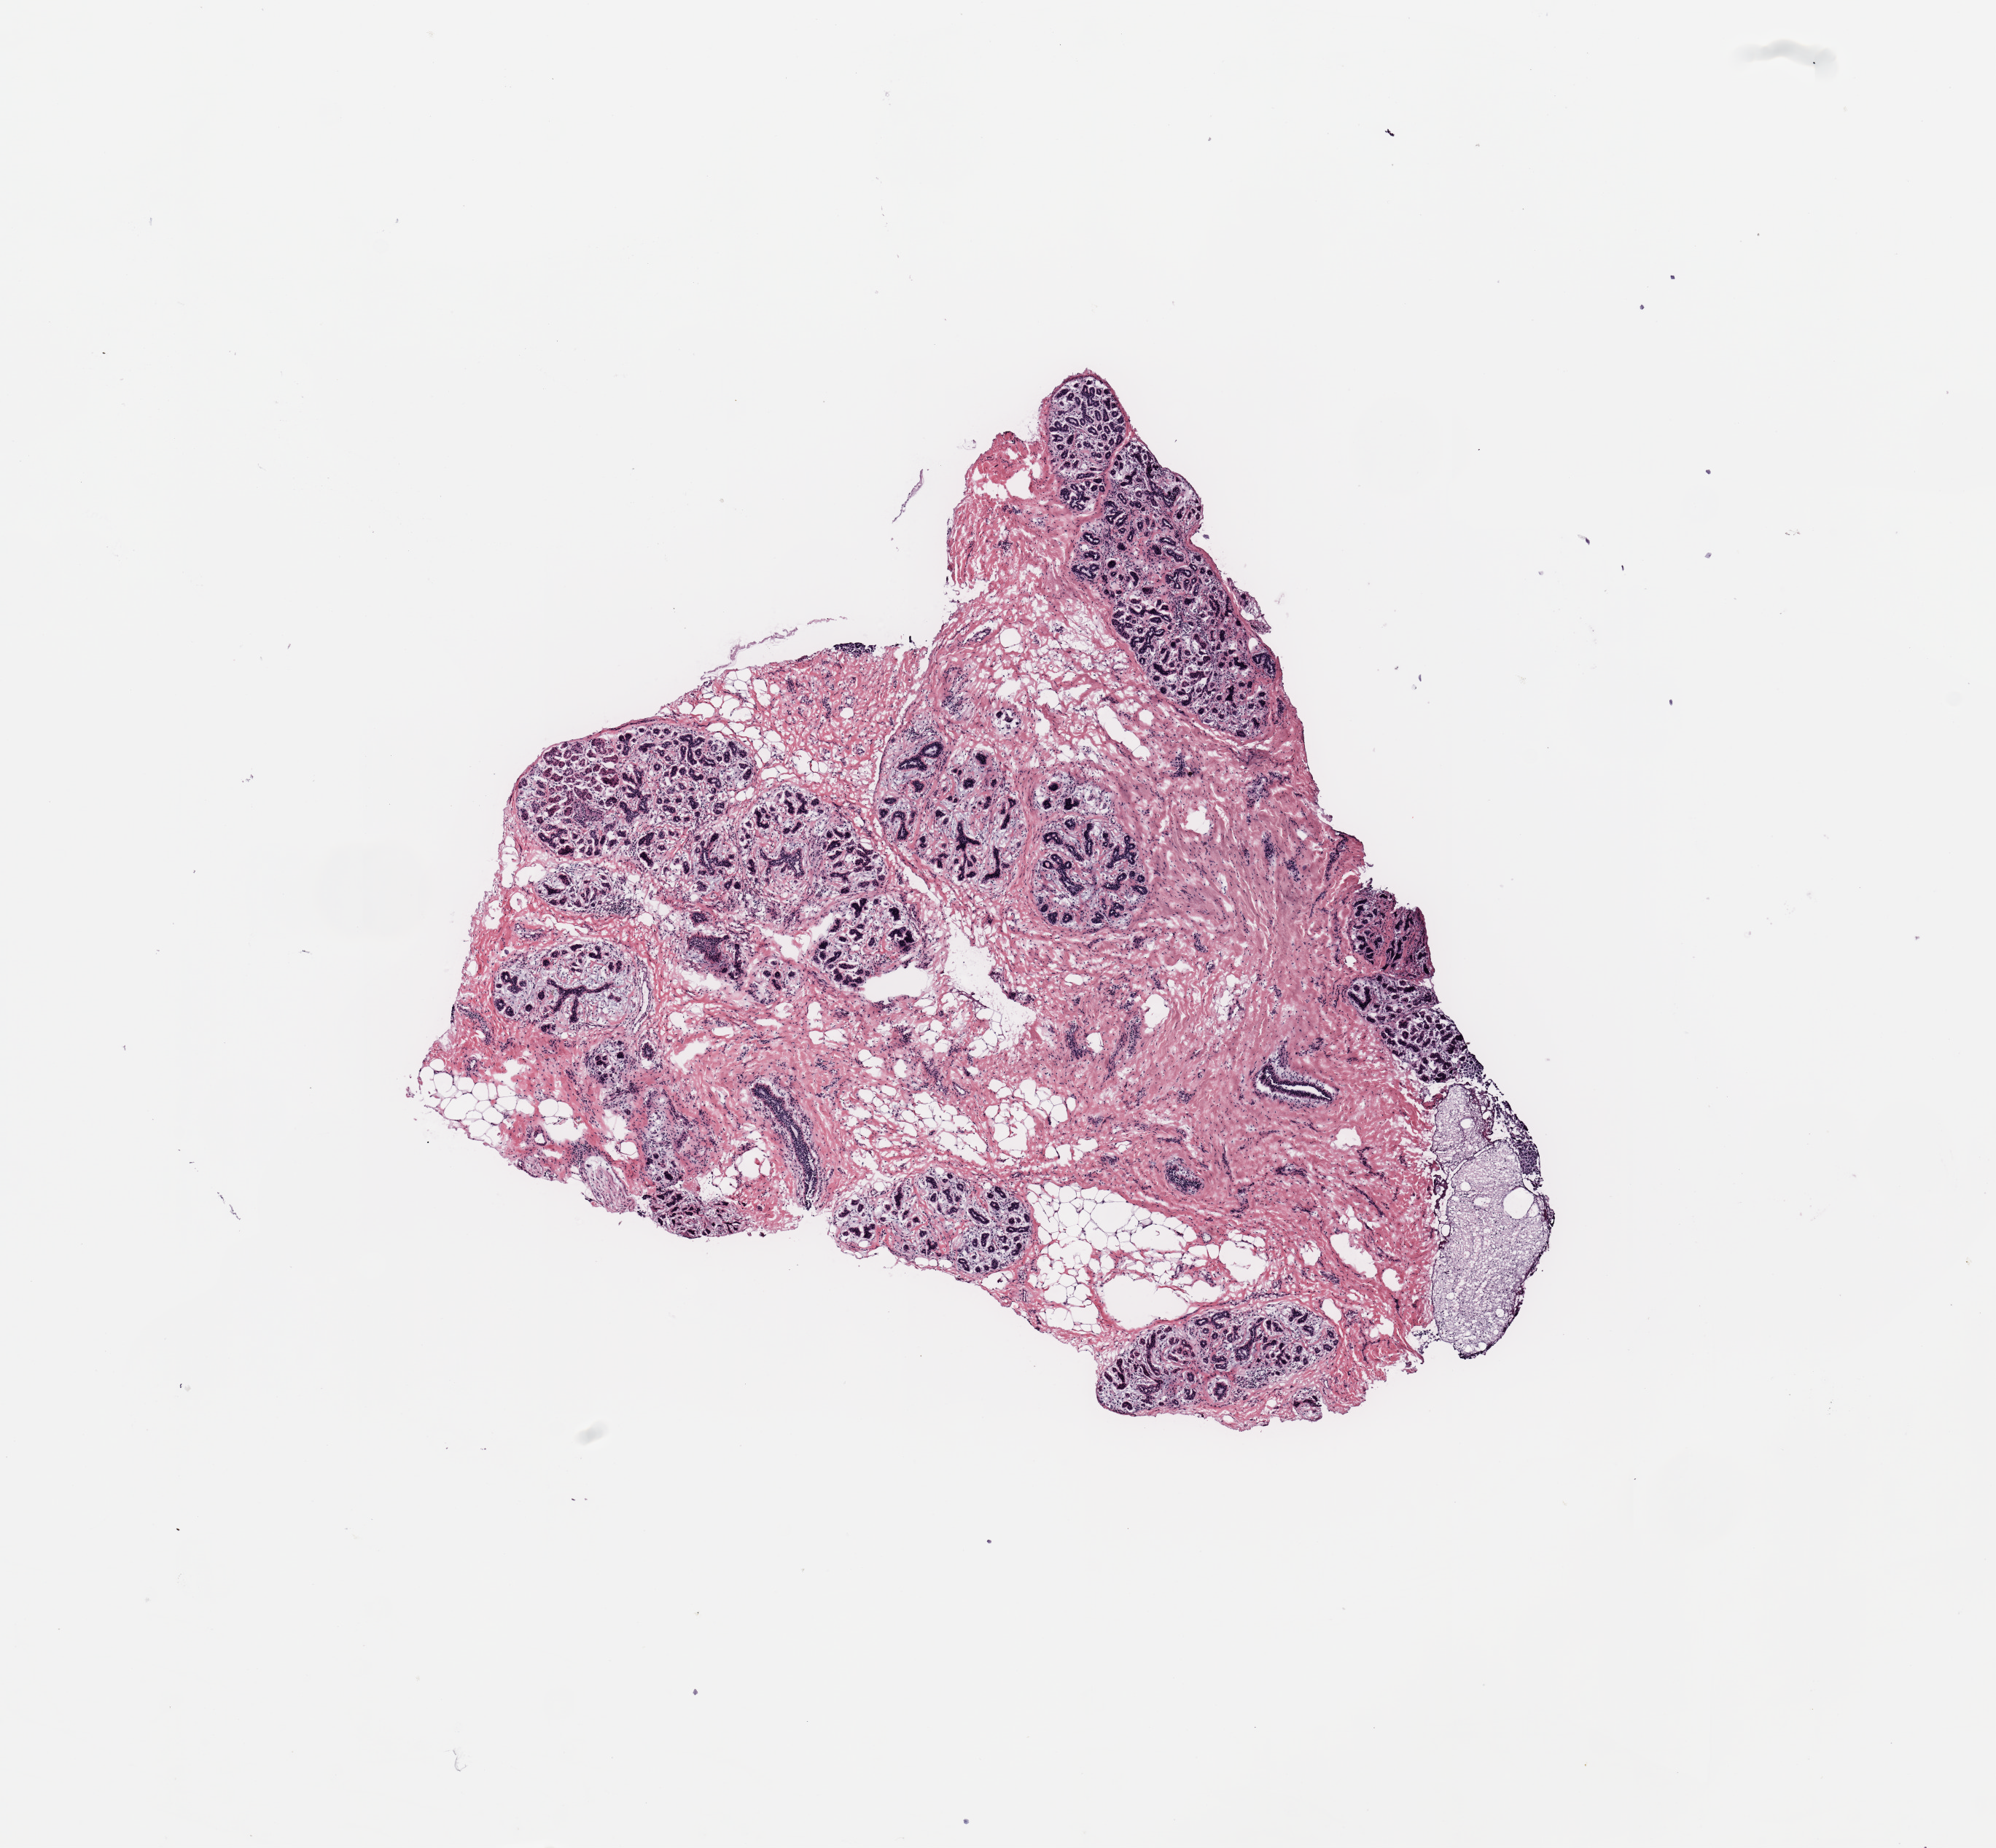
Hematoxylin and eosin (H&E) stained whole-slide image, low-resolution overview of the scanned area, about 10.8 x 10.0 mm (from a 20x scan). Breast, tissue type not recorded.
Patient diagnosis (cohort enrolment): breast cancer (breast).